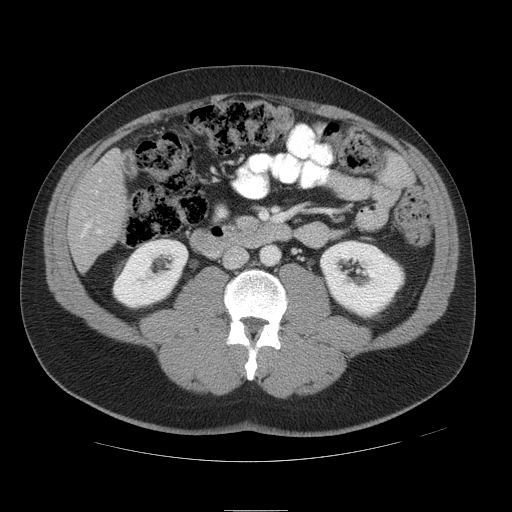
Contrast-enhanced abdominal CT, one axial slice; position 15 of 49 along the scan axis; 120 kVp; intravenous contrast given; soft-tissue window (W 400 / L 40 HU); 5 mm slice thickness; 512 × 512 image matrix, field of view 425 × 425 mm. Male patient, age 52 years. From the clinical record (not read from this slice): diagnosis: colorectal cancer liver metastases, imaged before liver resection; multiple liver metastases: yes; largest metastasis: 5.1 cm.
Outlined on this slice (outlined manually by an expert reader):
- hepatic veins: bounding box [x1, y1, x2, y2] px = [81, 223, 91, 237]
- liver: [69, 154, 125, 269]
- portal vein (with intrahepatic branches): [95, 160, 108, 234]